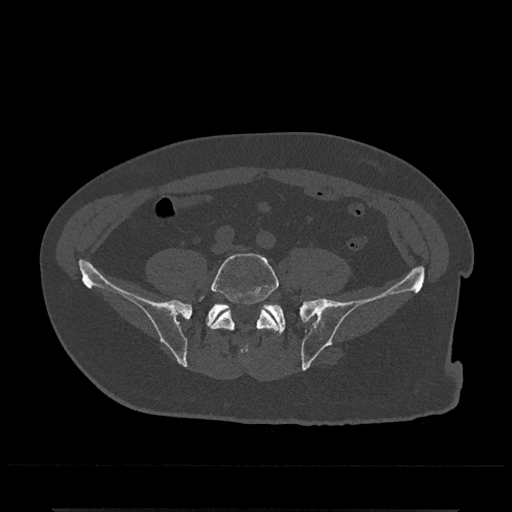
CT including the spine, one axial slice; slice 71 of 797 in the series (ordered by position); bone window (W 1800 / L 400 HU); 0.5 mm slice thickness; 512 × 512 image matrix, field of view 393 × 393 mm. Patient: male, 67 years. Case-level facts recorded for this patient, not image findings: primary cancer: prostate.
Structures marked on this image (semi-automatic segmentation, software-assisted and operator-edited):
- L5 vertebra: bounding box <199,253,280,358> (left, top, right, bottom; pixels)